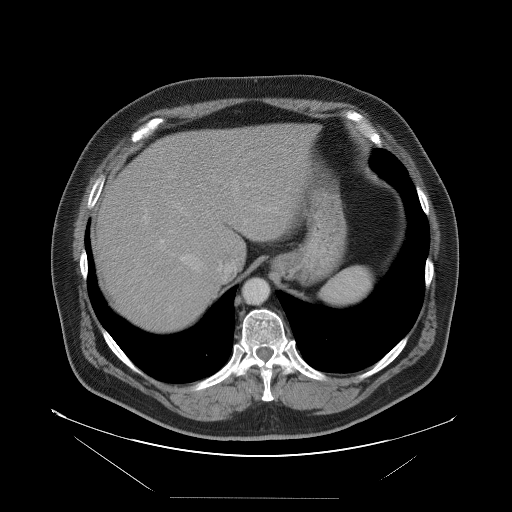
Contrast-enhanced abdominal CT, one axial slice; slice 79 of 114 in the series (ordered by position); 120 kVp; soft-tissue window (W 400 / L 40 HU); 5 mm slice thickness; 512 × 512 image matrix, field of view 500 × 500 mm. Male patient, age 61 years. Case-level facts recorded for this patient, not image findings: diagnosis: colorectal cancer liver metastases, imaged before liver resection; multiple liver metastases: no; largest metastasis: 6.5 cm; chemotherapy before resection: no.
Structures marked on this image (outlined manually by an expert reader):
- hepatic veins: bounding box (x1, y1, x2, y2) in pixels: (170, 181, 278, 281)
- liver: (92, 125, 315, 334)
- planned liver remnant (the part of the liver to remain after resection): (147, 124, 314, 265)
- portal vein (with intrahepatic branches): (143, 215, 165, 244)